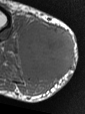
MRI of an extremity soft-tissue mass, one axial slice; position 21 of 47 along the scan axis; MR volume resampled by the dataset authors to the PET/CT grid (not the native acquisition matrix); 3.27 mm slice thickness; 85 × 114 image matrix, field of view 83 × 111 mm. Male patient. From the clinical record (not read from this slice): histological type: pleiomorphic liposarcoma; grade: high; site of the primary tumour: right calf.
Outlined on this slice (expert contour drawn on MRI and transferred to this co-registered scan by the dataset authors):
- gross tumour volume including surrounding oedema: bounding box (x1, y1, x2, y2) in pixels: (17, 16, 75, 95)
- gross tumour volume (mass): (19, 23, 75, 81)